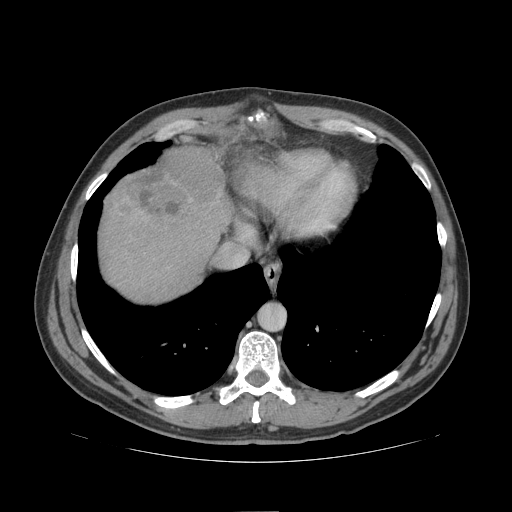
Contrast-enhanced abdominal CT (liver protocol), one axial slice; position 91 of 109 along the scan axis; reconstruction kernel STANDARD; 140 kVp; soft-tissue window (W 400 / L 40 HU); 512 × 512 image matrix. From the clinical record (not read from this slice): diagnosis: hepatocellular carcinoma (patient treated with transarterial chemoembolisation; whether this scan precedes or follows treatment is not stated here); TNM stage (as recorded): Stage-IIIB; Child-Pugh class: A.
Outlined on this slice (semi-automatic segmentation, software-assisted and operator-edited):
- liver parenchyma outside the tumour (the mass and vessels are separate outlines, so this box may not span the whole liver): box from (x=100, y=156) to (x=270, y=300) px
- mass: (x=105, y=145)–(x=225, y=216)